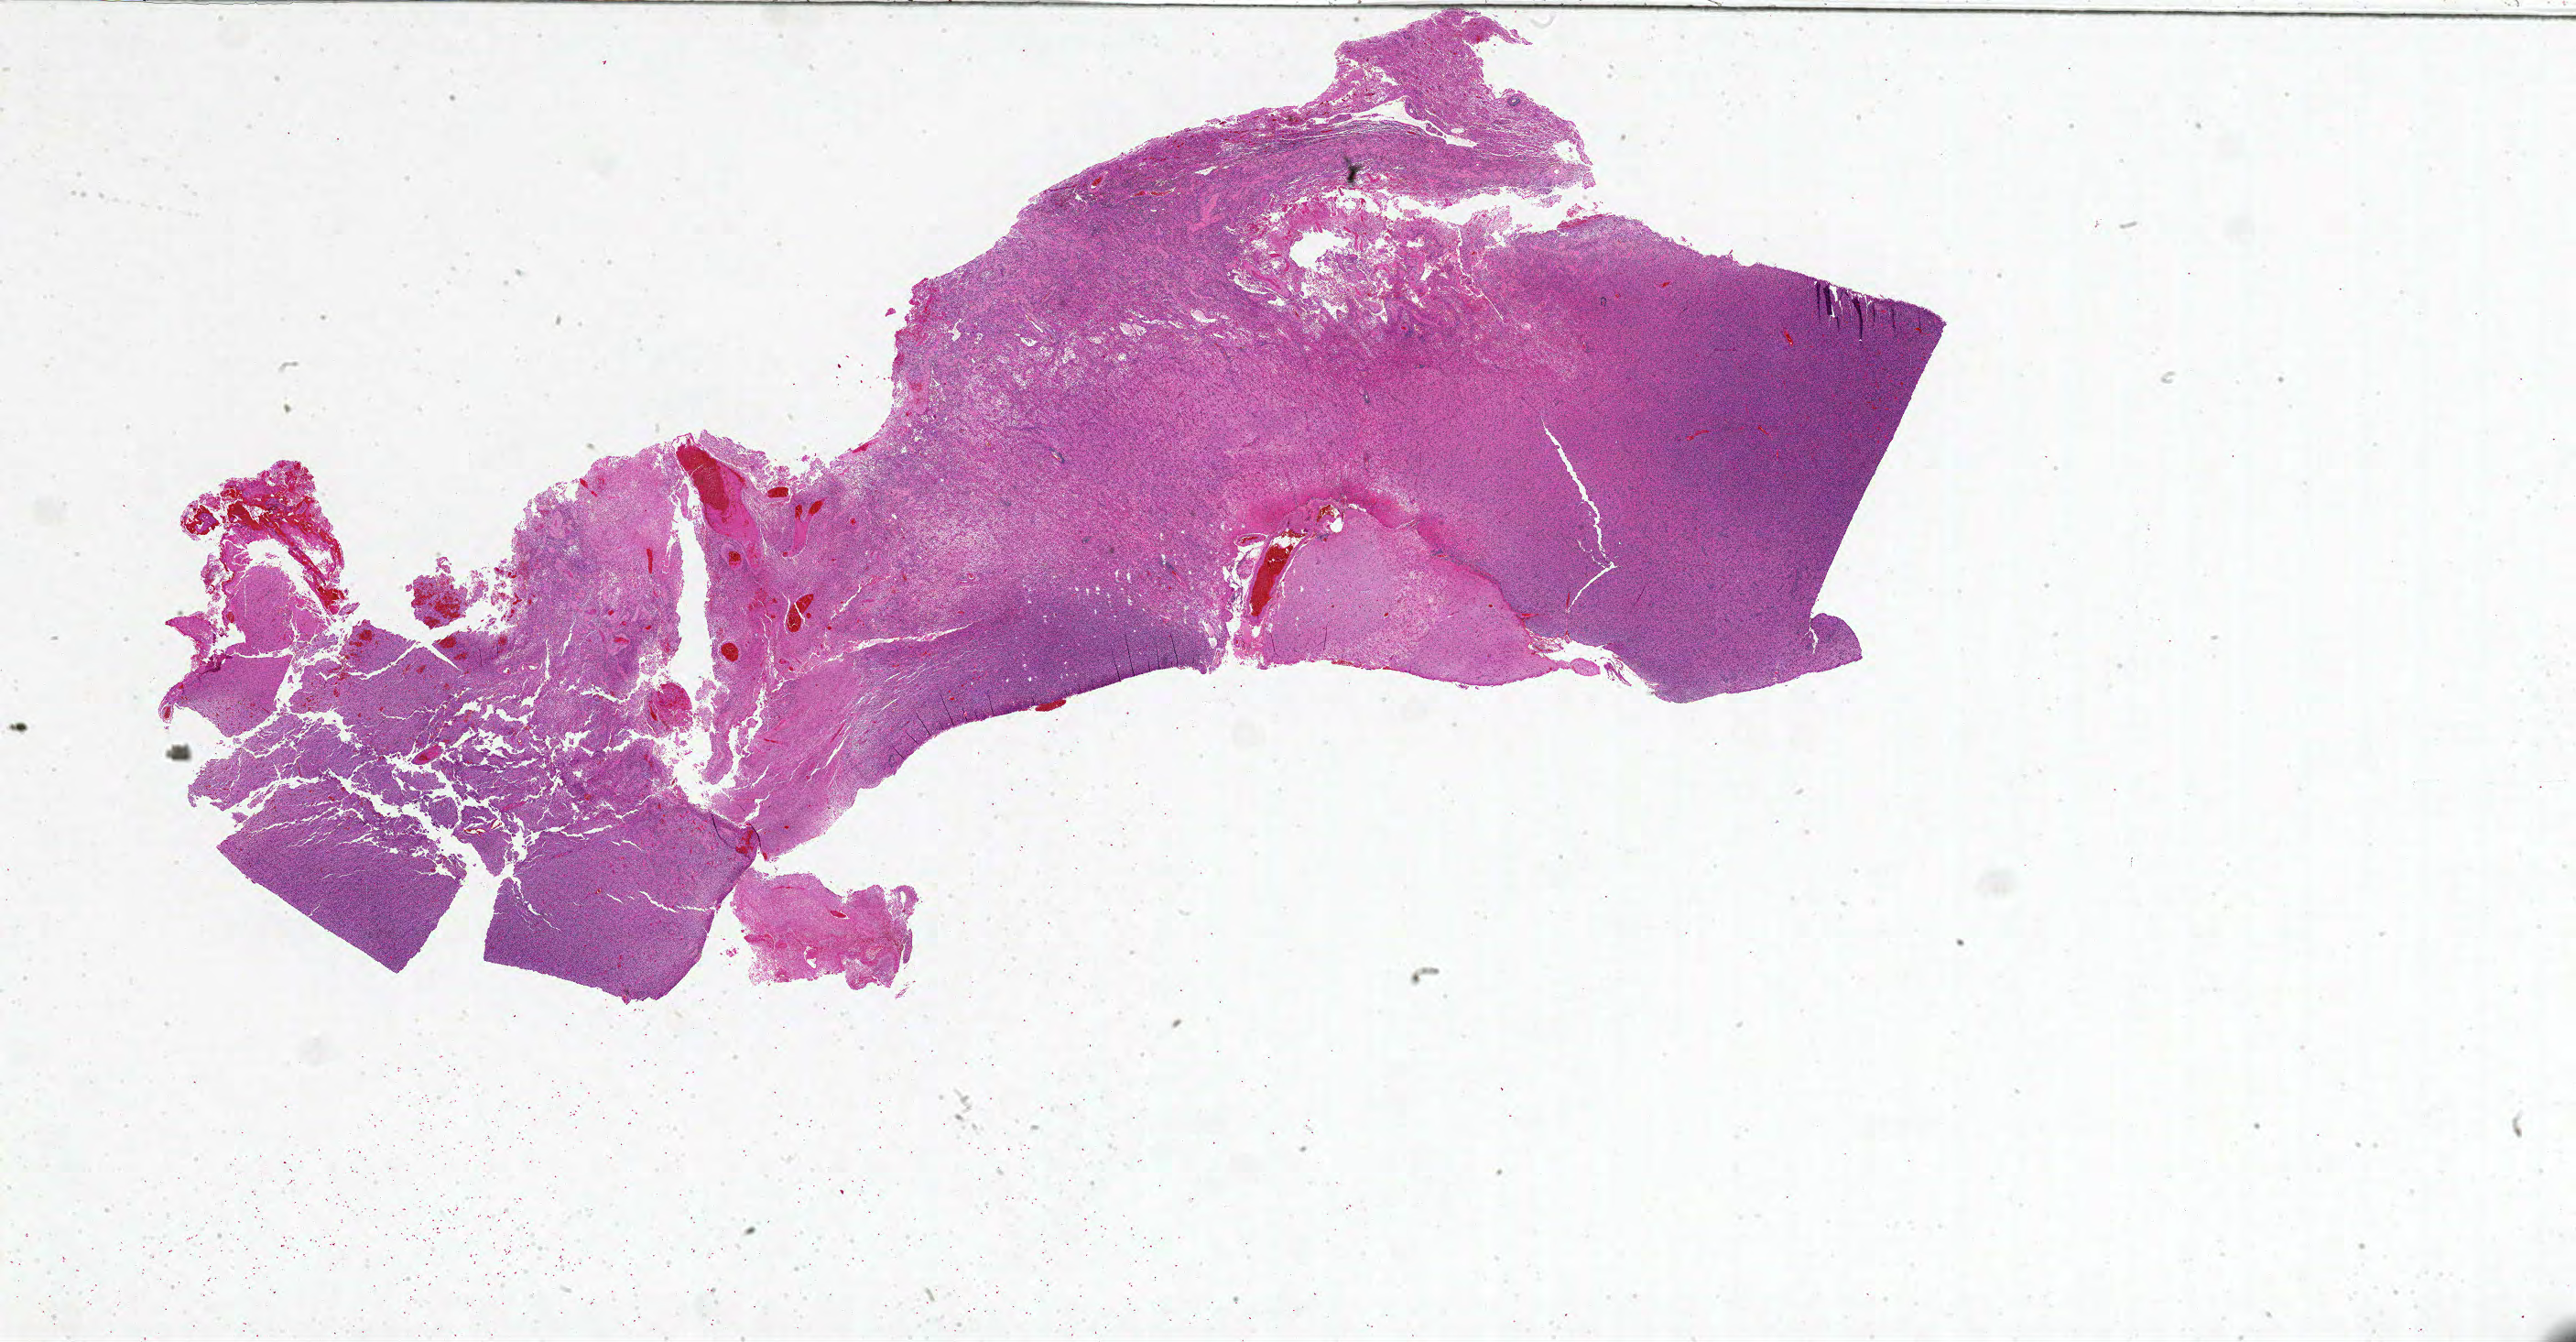
Digitized H&E-stained tissue section (whole slide) — low-resolution overview of the scanned area, about 45.0 x 23.4 mm (from a 20x scan); formalin-fixed paraffin-embedded (FFPE) diagnostic section; primary tumour sample from the brain. Male, age 60 years at initial diagnosis.
Histologic diagnosis: Glioblastoma.